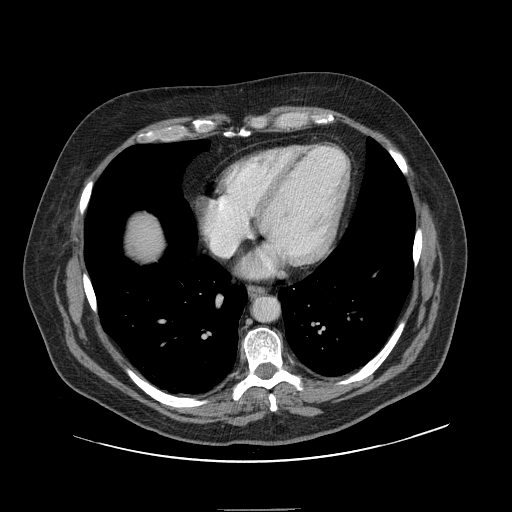
Contrast-enhanced abdominal CT, one axial slice. Slice 146 of 154 in the series (ordered by position). Intravenous contrast given. Soft-tissue window (W 400 / L 40 HU). 512 × 512 image matrix. Male patient, age 61 years. From the clinical record (not read from this slice): diagnosis: colorectal cancer liver metastases, imaged before liver resection; multiple liver metastases: yes; largest metastasis: 2.6 cm; disease in both lobes: yes.
Outlined on this slice (manually delineated by an expert):
- liver: bounding box [x1, y1, x2, y2] px = [131, 219, 161, 258]
- planned liver remnant (the part of the liver to remain after resection): [131, 218, 161, 258]